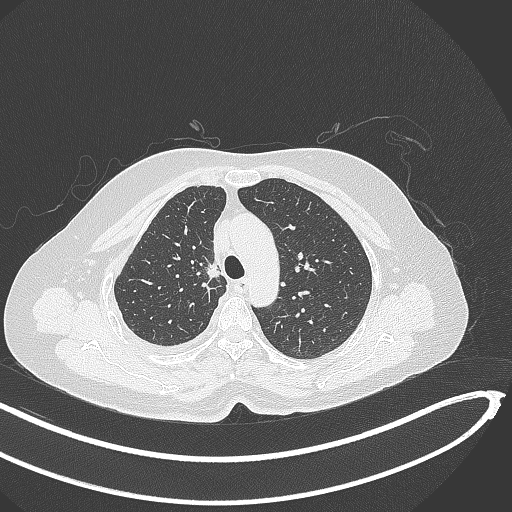
Chest CT, one axial slice; slice 279 of 345 in the series (ordered by position); reconstruction kernel B70f; lung window (W 1500 / L -600 HU); 1 mm slice thickness; 512 × 512 image matrix, field of view 400 × 400 mm. Patient: female, 64 years. From the clinical record (not read from this slice): clinical TNM (as recorded): T1b N0 M1.
Annotated regions visible in this slice (bounding box drawn by a radiologist):
- lung tumour (recorded histology: adenocarcinoma): bounding box (x1, y1, x2, y2) in pixels: (203, 256, 223, 282)